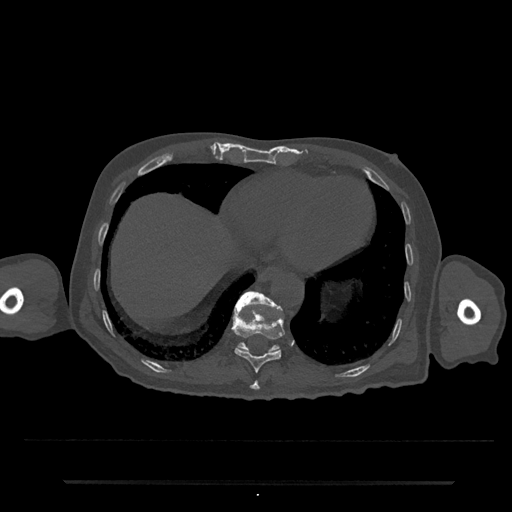
CT including the spine, one axial slice. Slice 299 of 797 in the series (ordered by position). Bone window (W 1800 / L 400 HU). 512 × 512 image matrix. Patient: male, 74 years. Case-level facts recorded for this patient, not image findings: primary cancer: prostate.
Annotated regions visible in this slice (semi-automatic segmentation, software-assisted and operator-edited):
- T10 vertebra: bounding box (x1, y1, x2, y2) in pixels: (232, 307, 285, 373)
- T11 vertebra: (234, 291, 283, 352)
- T9 vertebra: (250, 381, 260, 391)